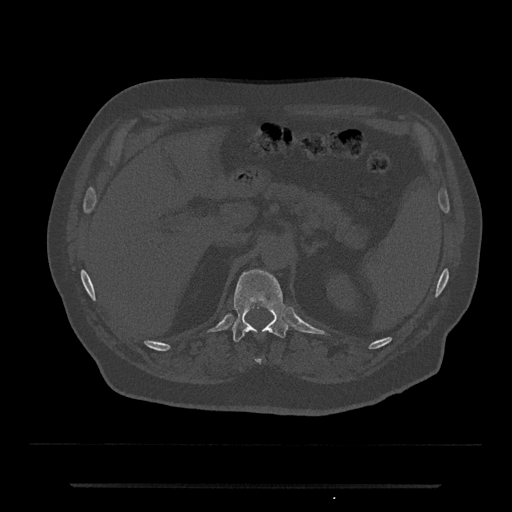
CT including the spine, one axial slice; position 599 of 797 along the scan axis; reconstruction kernel Br40s/3; 120 kVp; bone window (W 1800 / L 400 HU); 0.5 mm slice thickness; 512 × 512 image matrix, field of view 434 × 434 mm. Male patient, age 80 years. From the clinical record (not read from this slice): primary cancer: prostate.
Structures marked on this image (semi-automatically segmented with operator editing):
- T11 vertebra: box from (x=256, y=360) to (x=261, y=363) px
- T12 vertebra: (x=231, y=269)–(x=289, y=342)